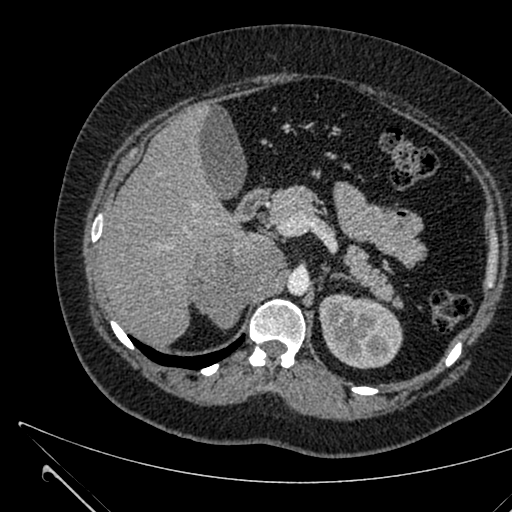
Contrast-enhanced abdominal CT, one axial slice. Position 422 of 731 along the scan axis. 120 kVp. Intravenous contrast given. Soft-tissue window (W 400 / L 40 HU). 1 mm slice thickness. 512 × 512 image matrix, field of view 376 × 376 mm. Female patient, age 36 years. Case-level facts recorded for this patient, not image findings: diagnosis: adrenocortical carcinoma; tumour side: right adrenal; tumour size at pathology: 10 cm; Ki-67 index: 20 %; stage (as recorded): 4.
Structures marked on this image (semi-automatically segmented with operator editing):
- mass: bounding box <188,234,286,326> (left, top, right, bottom; pixels)